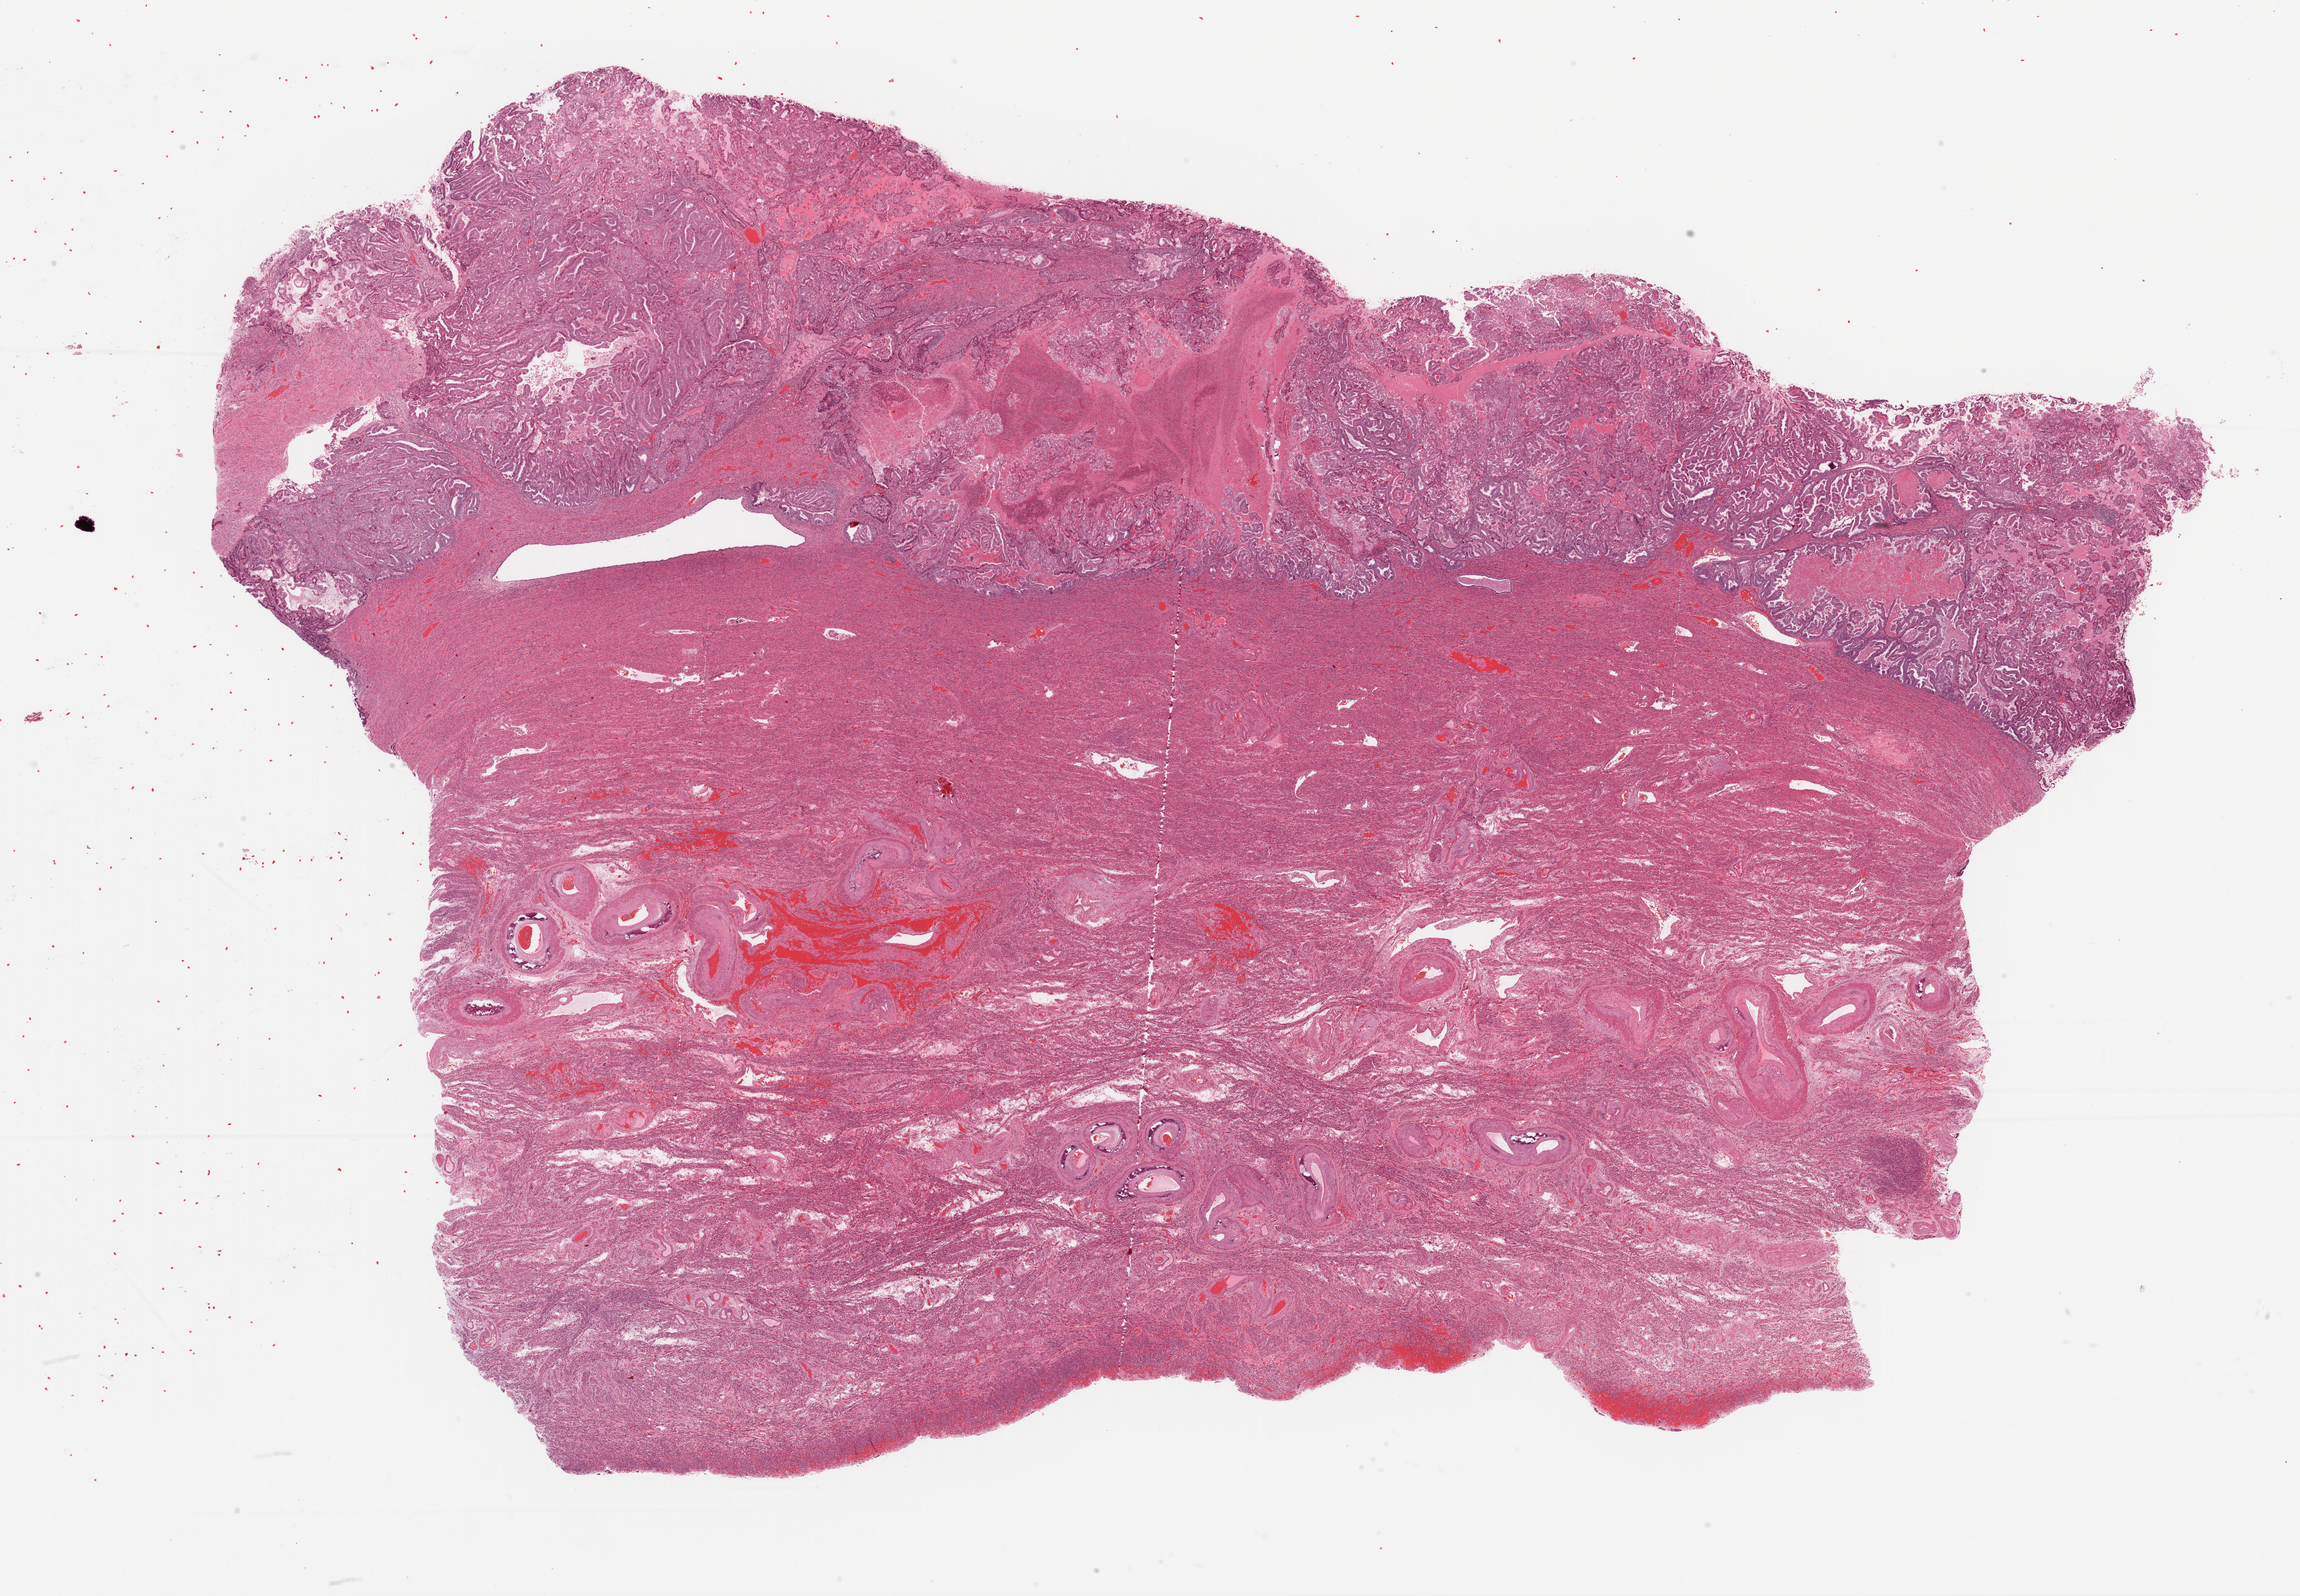
Whole-slide histology image, Hematoxylin and eosin (H&E) stained, whole scanned area (about 27.7 x 19.2 mm, acquisition: 40x scan) shown as a low-resolution overview; FFPE section; uterus, primary tumour sample. Female, age 82 years at initial diagnosis. Histologic grade: G2 (moderately differentiated).
Pathologic diagnosis: Endometrioid adenocarcinoma, NOS (endometrium). FIGO stage: IIIA.